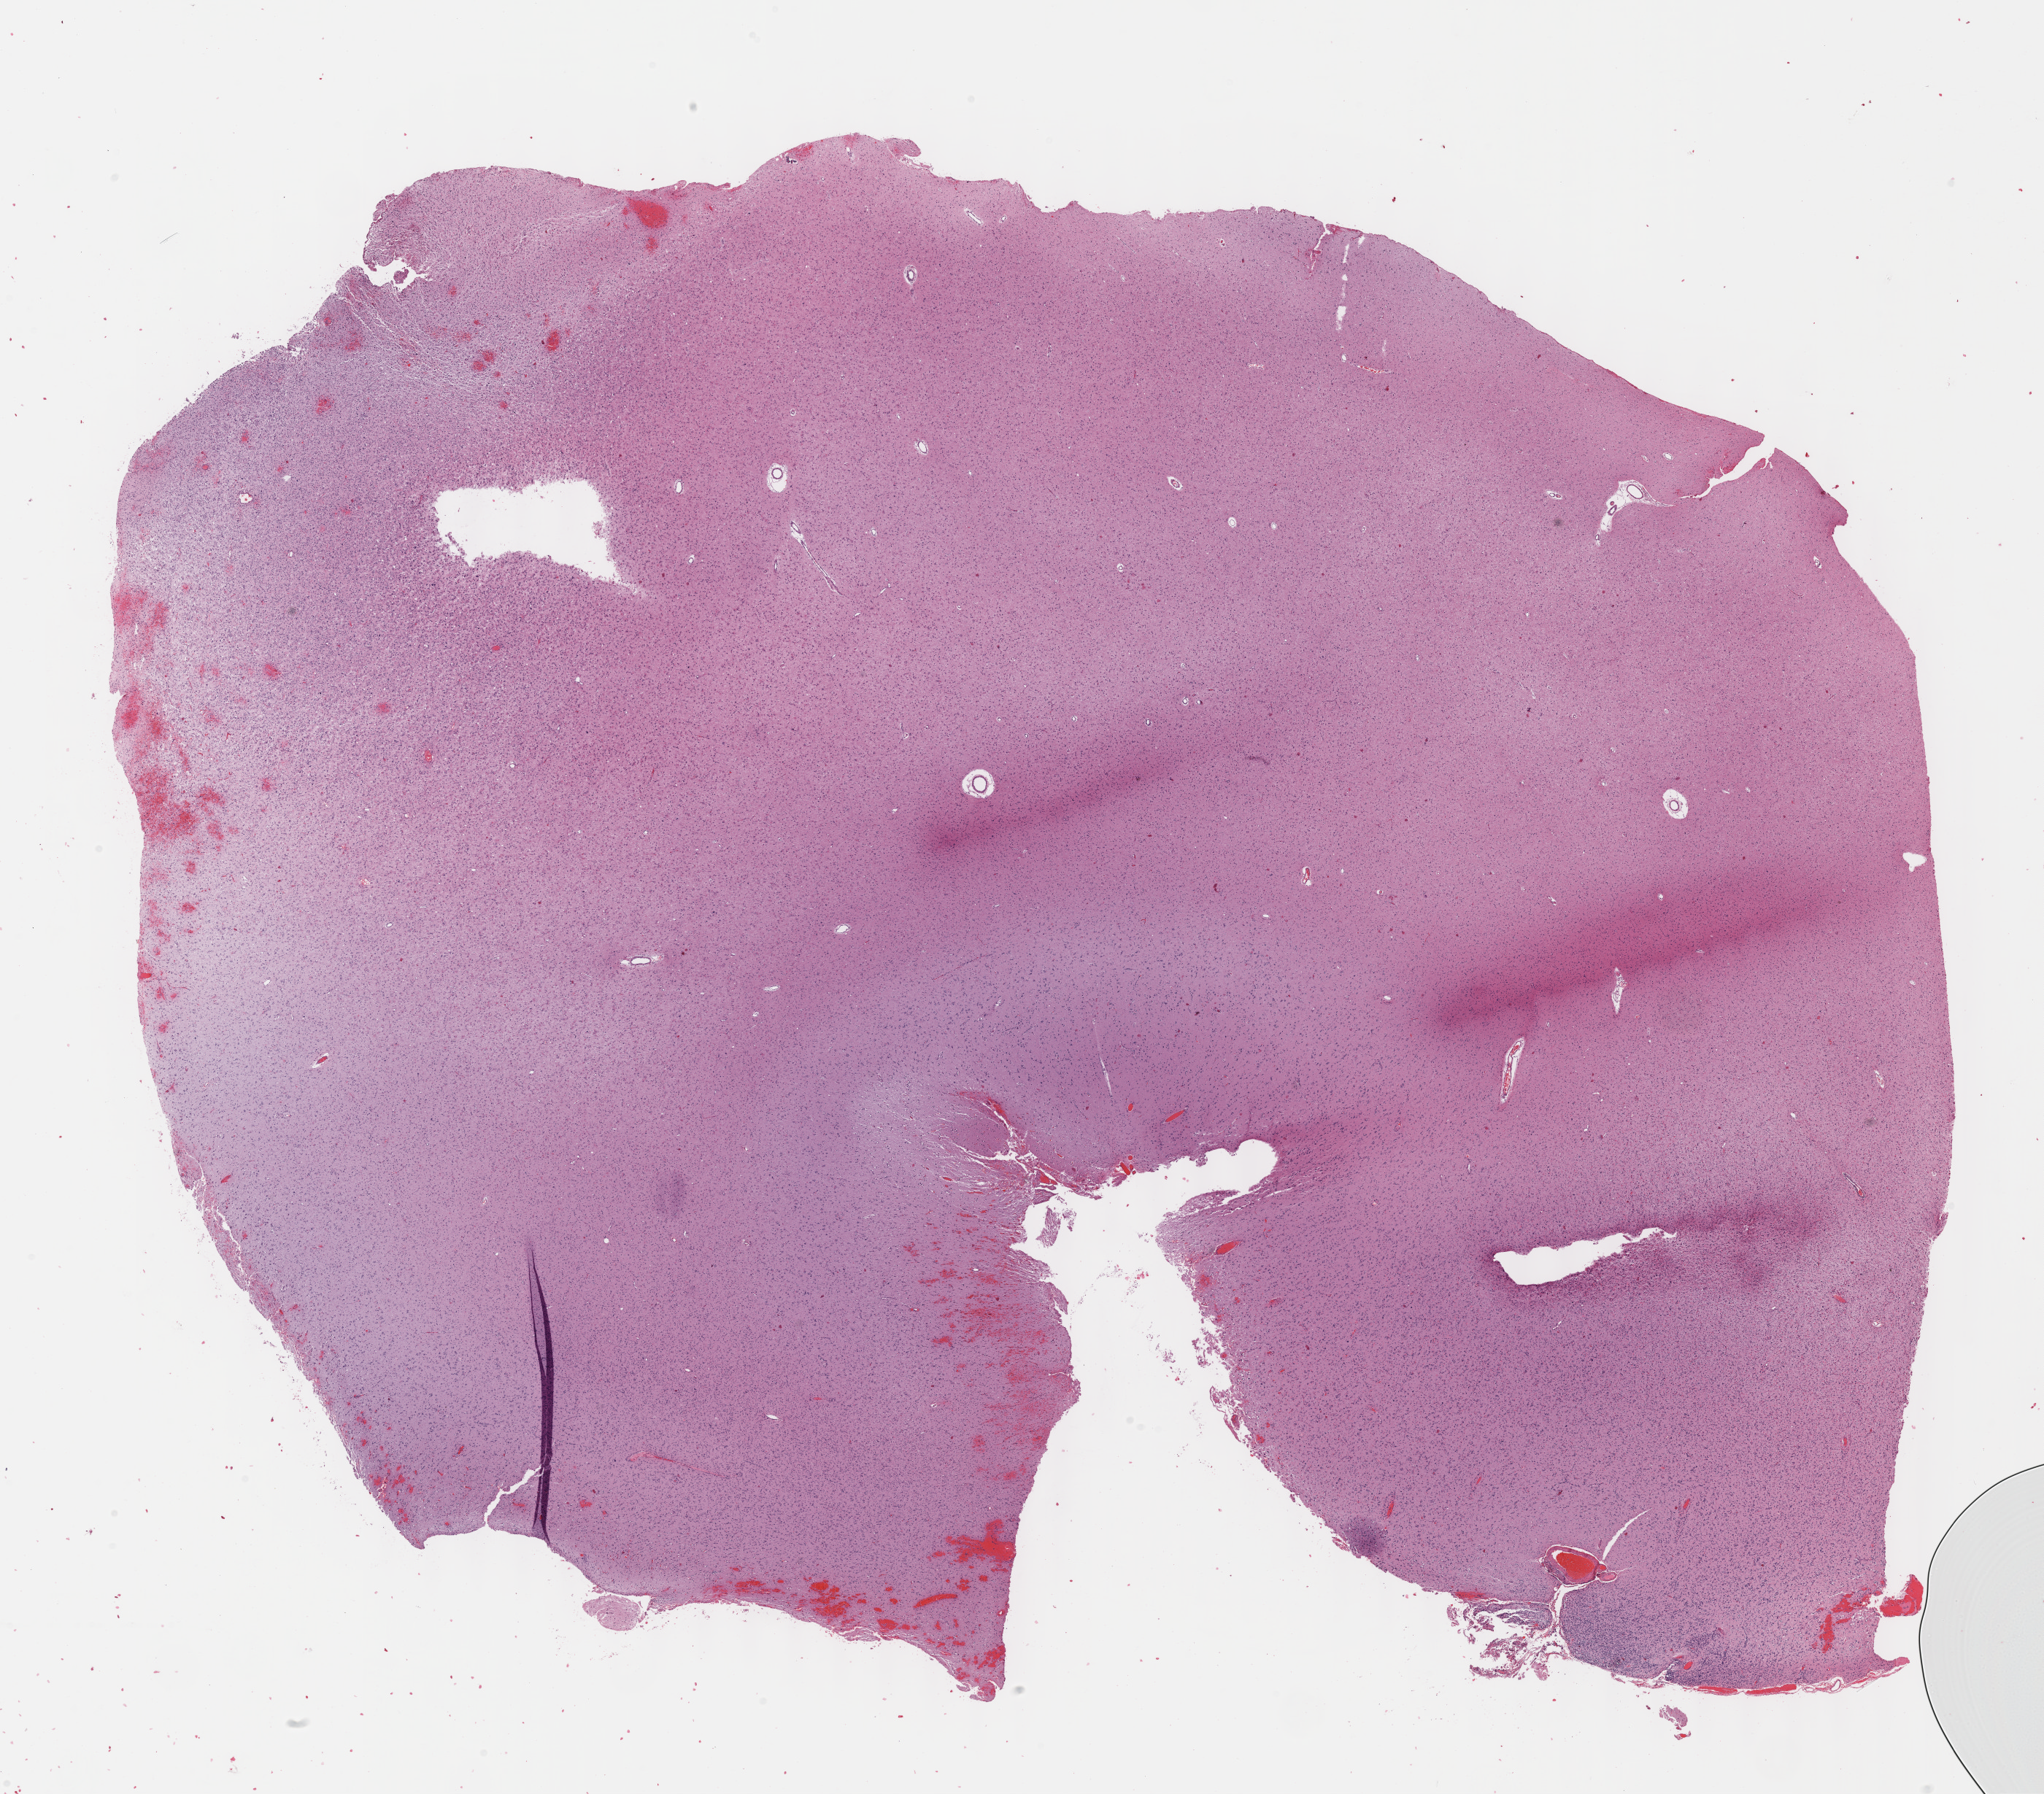
H&E-stained whole-slide image, shown as a low-resolution overview of the whole scanned area (about 22.6 x 19.9 mm, from a 40x scan), formalin-fixed paraffin-embedded (FFPE) diagnostic section, brain, primary tumour sample. Patient: female, age at initial diagnosis 30 years.
Histologic diagnosis: Astrocytoma, anaplastic (cerebrum).